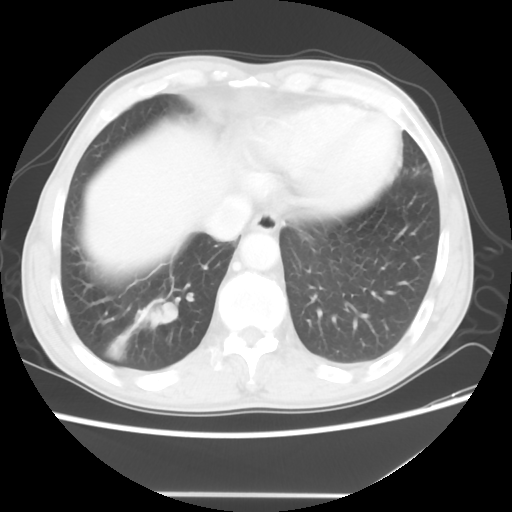
Chest CT, one axial slice. Position 12 of 56 along the scan axis. 120 kVp. Lung window (W 1500 / L -600 HU). 5 mm slice thickness. 512 × 512 image matrix, field of view 344 × 344 mm. Male patient, age 65 years. Case-level facts recorded for this patient, not image findings: clinical TNM (as recorded): T1c N3 M0; histopathological grade: G3.
Outlined on this slice (bounding box drawn by a radiologist):
- lung tumour (recorded histology: small cell carcinoma): bounding box (x1, y1, x2, y2) in pixels: (139, 299, 180, 326)